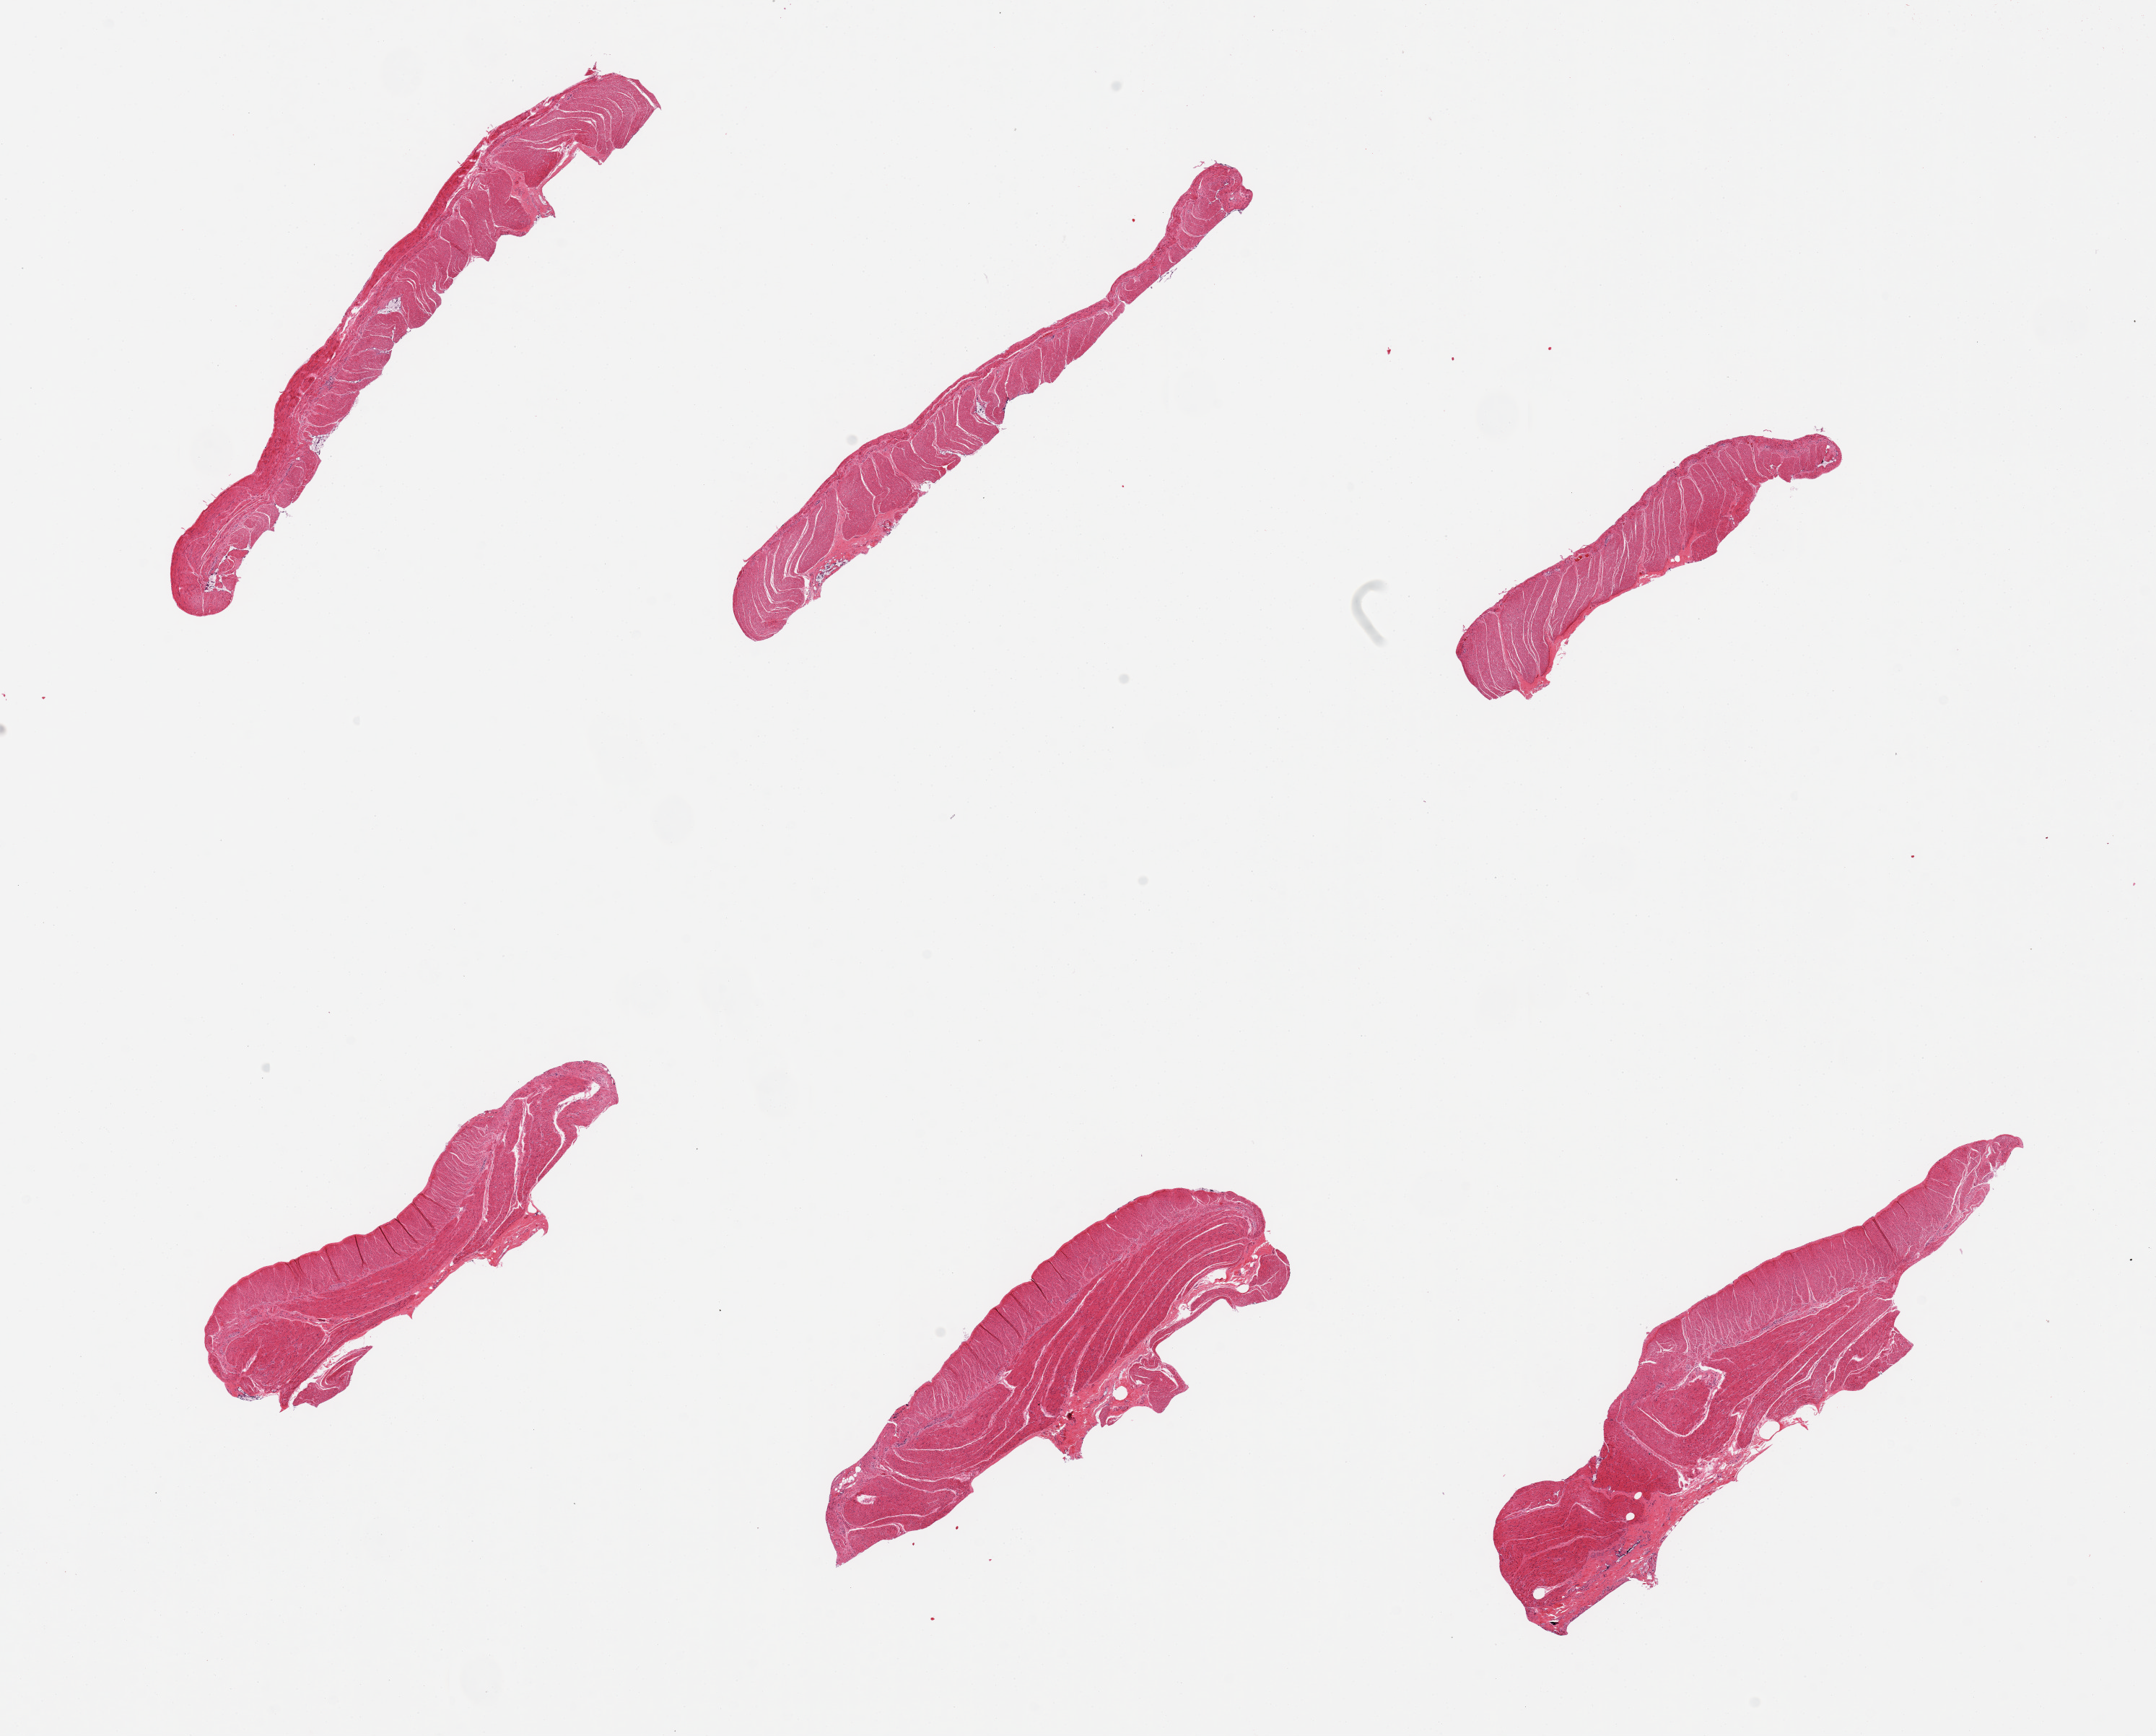
Digitized hematoxylin and eosin (H&E)-stained section, a low-resolution overview of the entire scanned area, about 23.6 x 19.0 mm, PAXgene-fixed paraffin-embedded (PFPE) section, target tissue: sigmoid colon, tissue donor sample. Donor: male.
Review note (as recorded): 6 pieces, all muscularis.